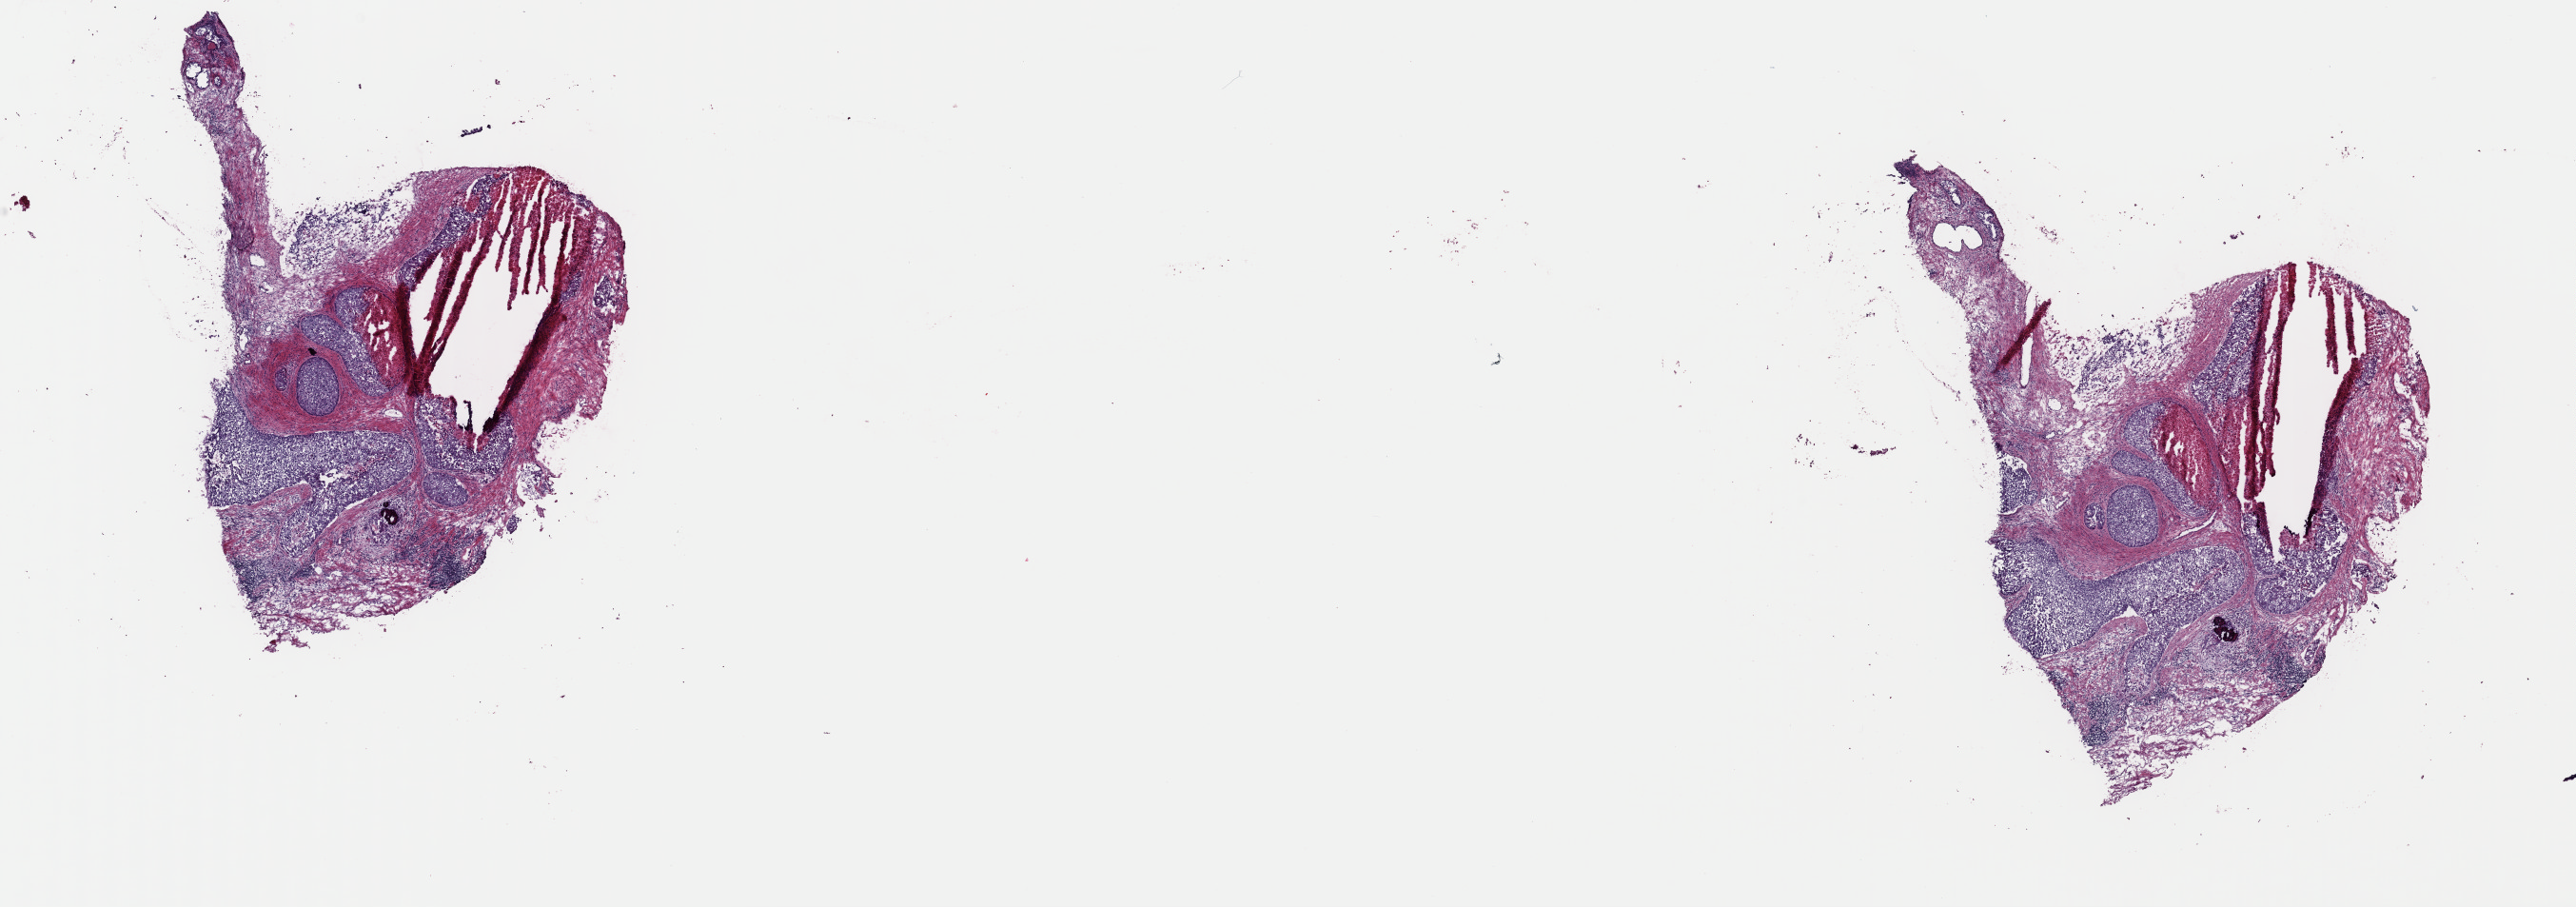
Whole-slide histology image, Hematoxylin and eosin (H&E) stained, low-resolution overview of the scanned area, about 21.4 x 7.5 mm (acquisition: 40x scan). Frozen section from the top of the tissue portion. Sample: primary tumour, bladder. Male patient; age at initial diagnosis 87 years. Histologic grade: high grade. Pathologist review of this section (percent, as recorded): tumour cells 65%, tumour nuclei 75%, normal cells 15%, stromal cells 0%, necrosis 20%. Inflammatory infiltration, as recorded: lymphocyte infiltration 5%, monocyte infiltration 1%, neutrophil infiltration 0%.
Pathologic diagnosis: Transitional cell carcinoma. TNM: T4a N0 MX. AJCC pathologic stage: III (7th edition).